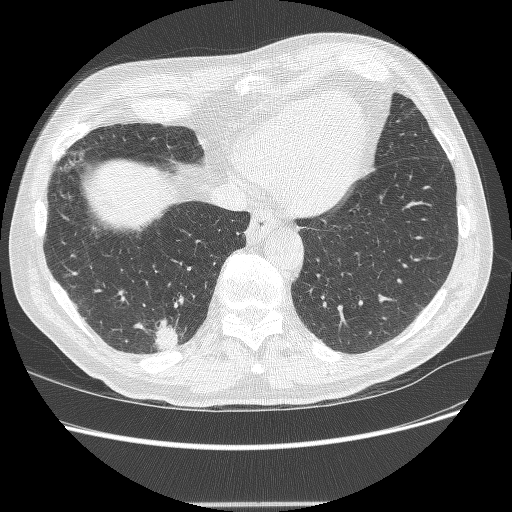
Axial slice from a low-dose chest CT screening exam. Second screening round (one year after baseline). Lung window (W 1500 / L -600 HU). 1.25 mm slice thickness. Lung (sharp) reconstruction kernel (BONE). 120 kVp. Slice 61 of 245 in the series. 512 × 512 image matrix. Male, age 71 years at enrolment.
Lesion marked by an expert reader, bounding box <137,321,187,359> (left, top, right, bottom; pixels). The screening reader recorded 5 non-calcified nodules or masses ≥4 mm on this exam (right lower lobe, right lower lobe, right upper lobe, right upper lobe, right upper lobe); which of them this box marks is not recorded. Later outcome: lung cancer diagnosed 7 days after this screen — squamous cell carcinoma, NOS, right lower lobe, moderately differentiated (G2), stage IA (AJCC 6th edition), 27 mm at pathology.